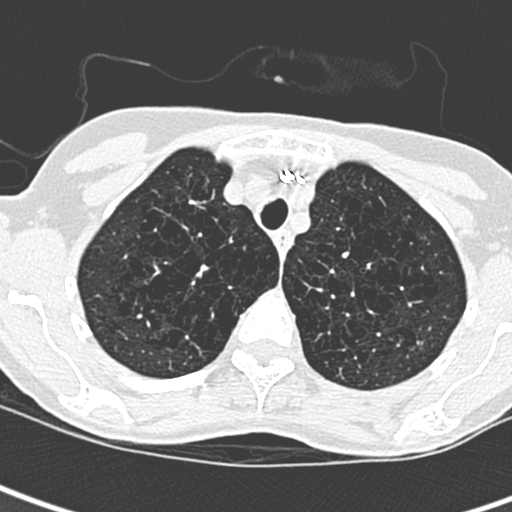
Low-dose screening chest CT, axial slice, baseline annual screen, lung window (W 1500 / L -600 HU), 1.3 mm slice thickness, lung (sharp) reconstruction kernel (D), 120 kVp, slice 51 of 259 in the series, 512 × 512 image matrix, field of view 275 × 275 mm. Female participant, aged 71 years at enrolment. Current smoker at enrolment.
• Expert-annotated lung lesion, bounding box [x1, y1, x2, y2] px = [398, 325, 436, 365].
• No non-calcified nodule or mass ≥4 mm was recorded by the screening reader at this exam.
• Lung cancer was diagnosed 975 days after this screen (after the third annual screen): adenocarcinoma, NOS, left upper lobe, moderately differentiated (G2), stage IA (AJCC 6th edition), 12 mm at pathology.